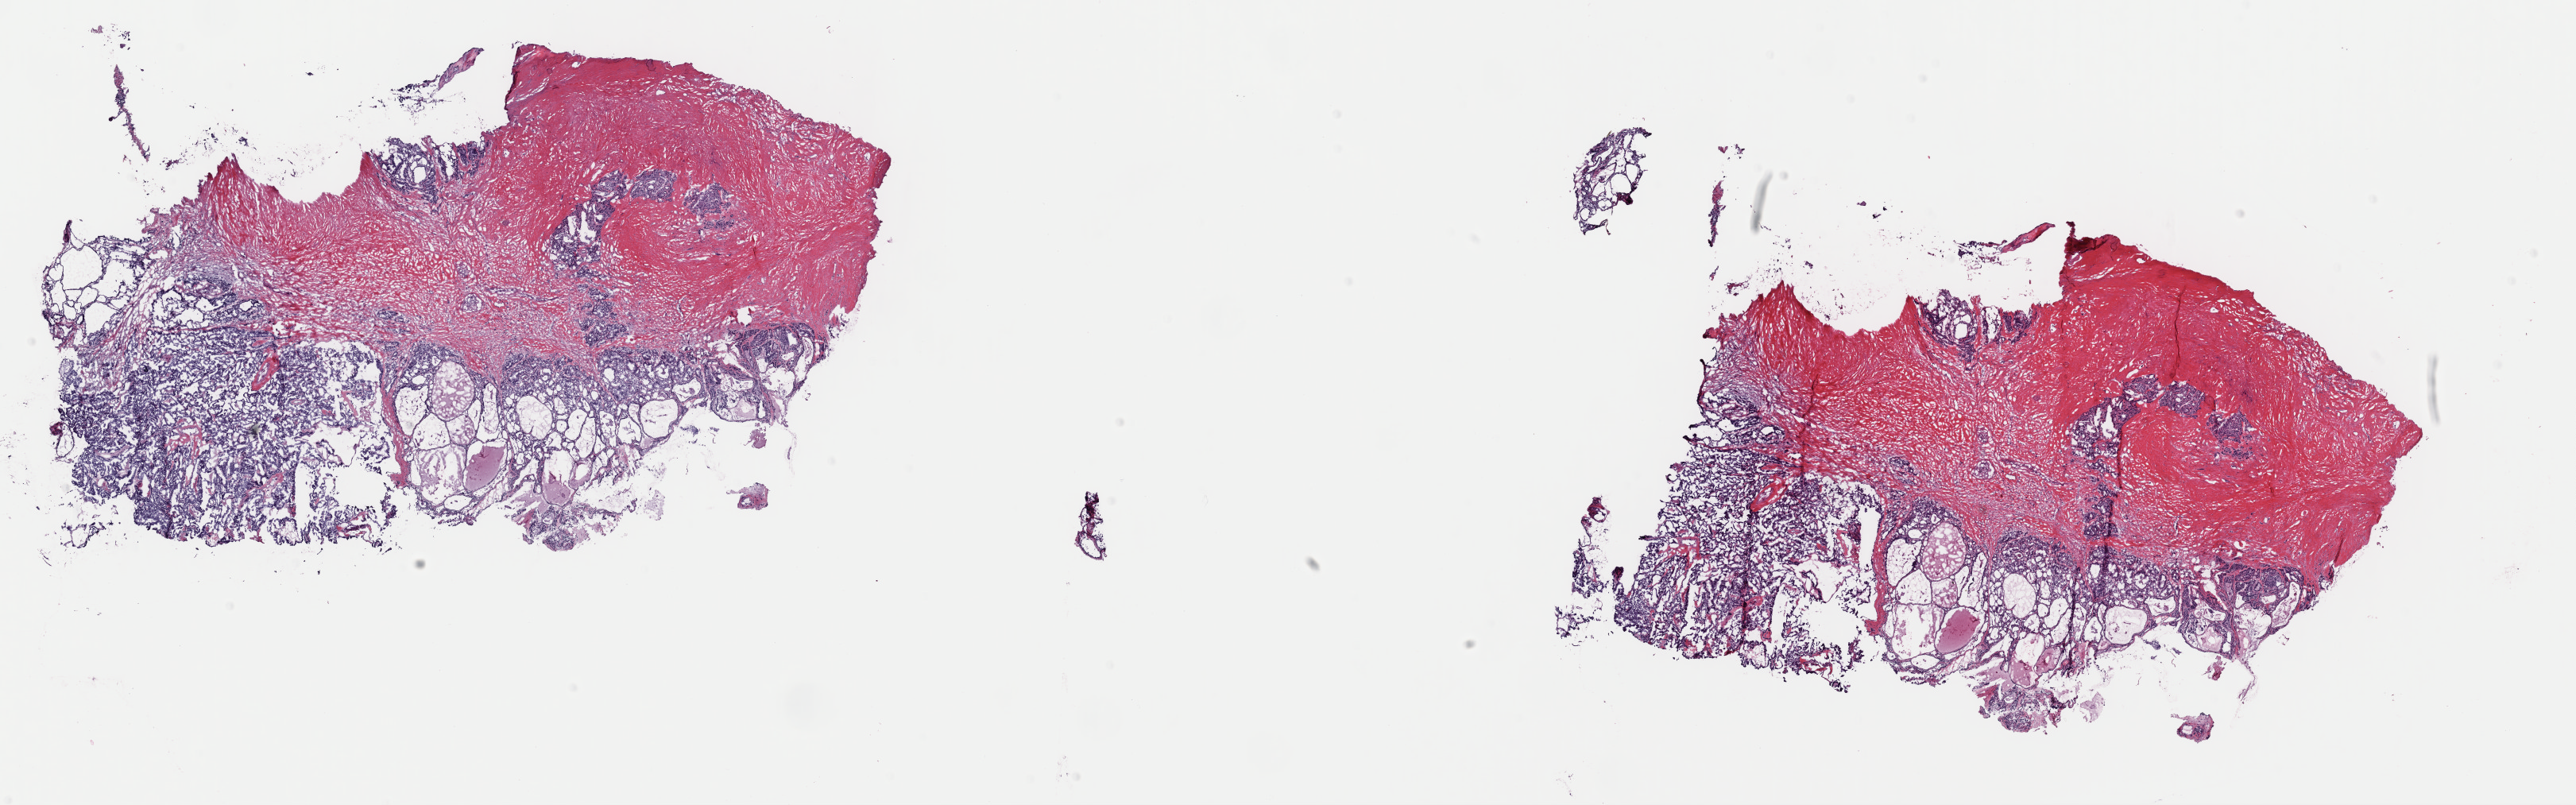
Digitized Hematoxylin and eosin (H&E) stained tissue section (whole slide), low-resolution overview of the scanned area, about 25.6 x 8.0 mm. Frozen section from the top of the tissue portion. Thyroid, primary tumour sample. Female, age 47 years at initial diagnosis. Pathologist review of this section (percent, as recorded): tumour cells 50%, tumour nuclei 90%, normal cells 10%, stromal cells 40%, necrosis 0%. Infiltration values recorded for this section: lymphocyte infiltration 0%, monocyte infiltration 1%, neutrophil infiltration 0%.
AJCC pathologic stage: III (6th edition). Laterality: right. Lymph nodes positive (case pathology): 2 of 6 examined. Histologic diagnosis: Papillary adenocarcinoma, NOS (thyroid gland).